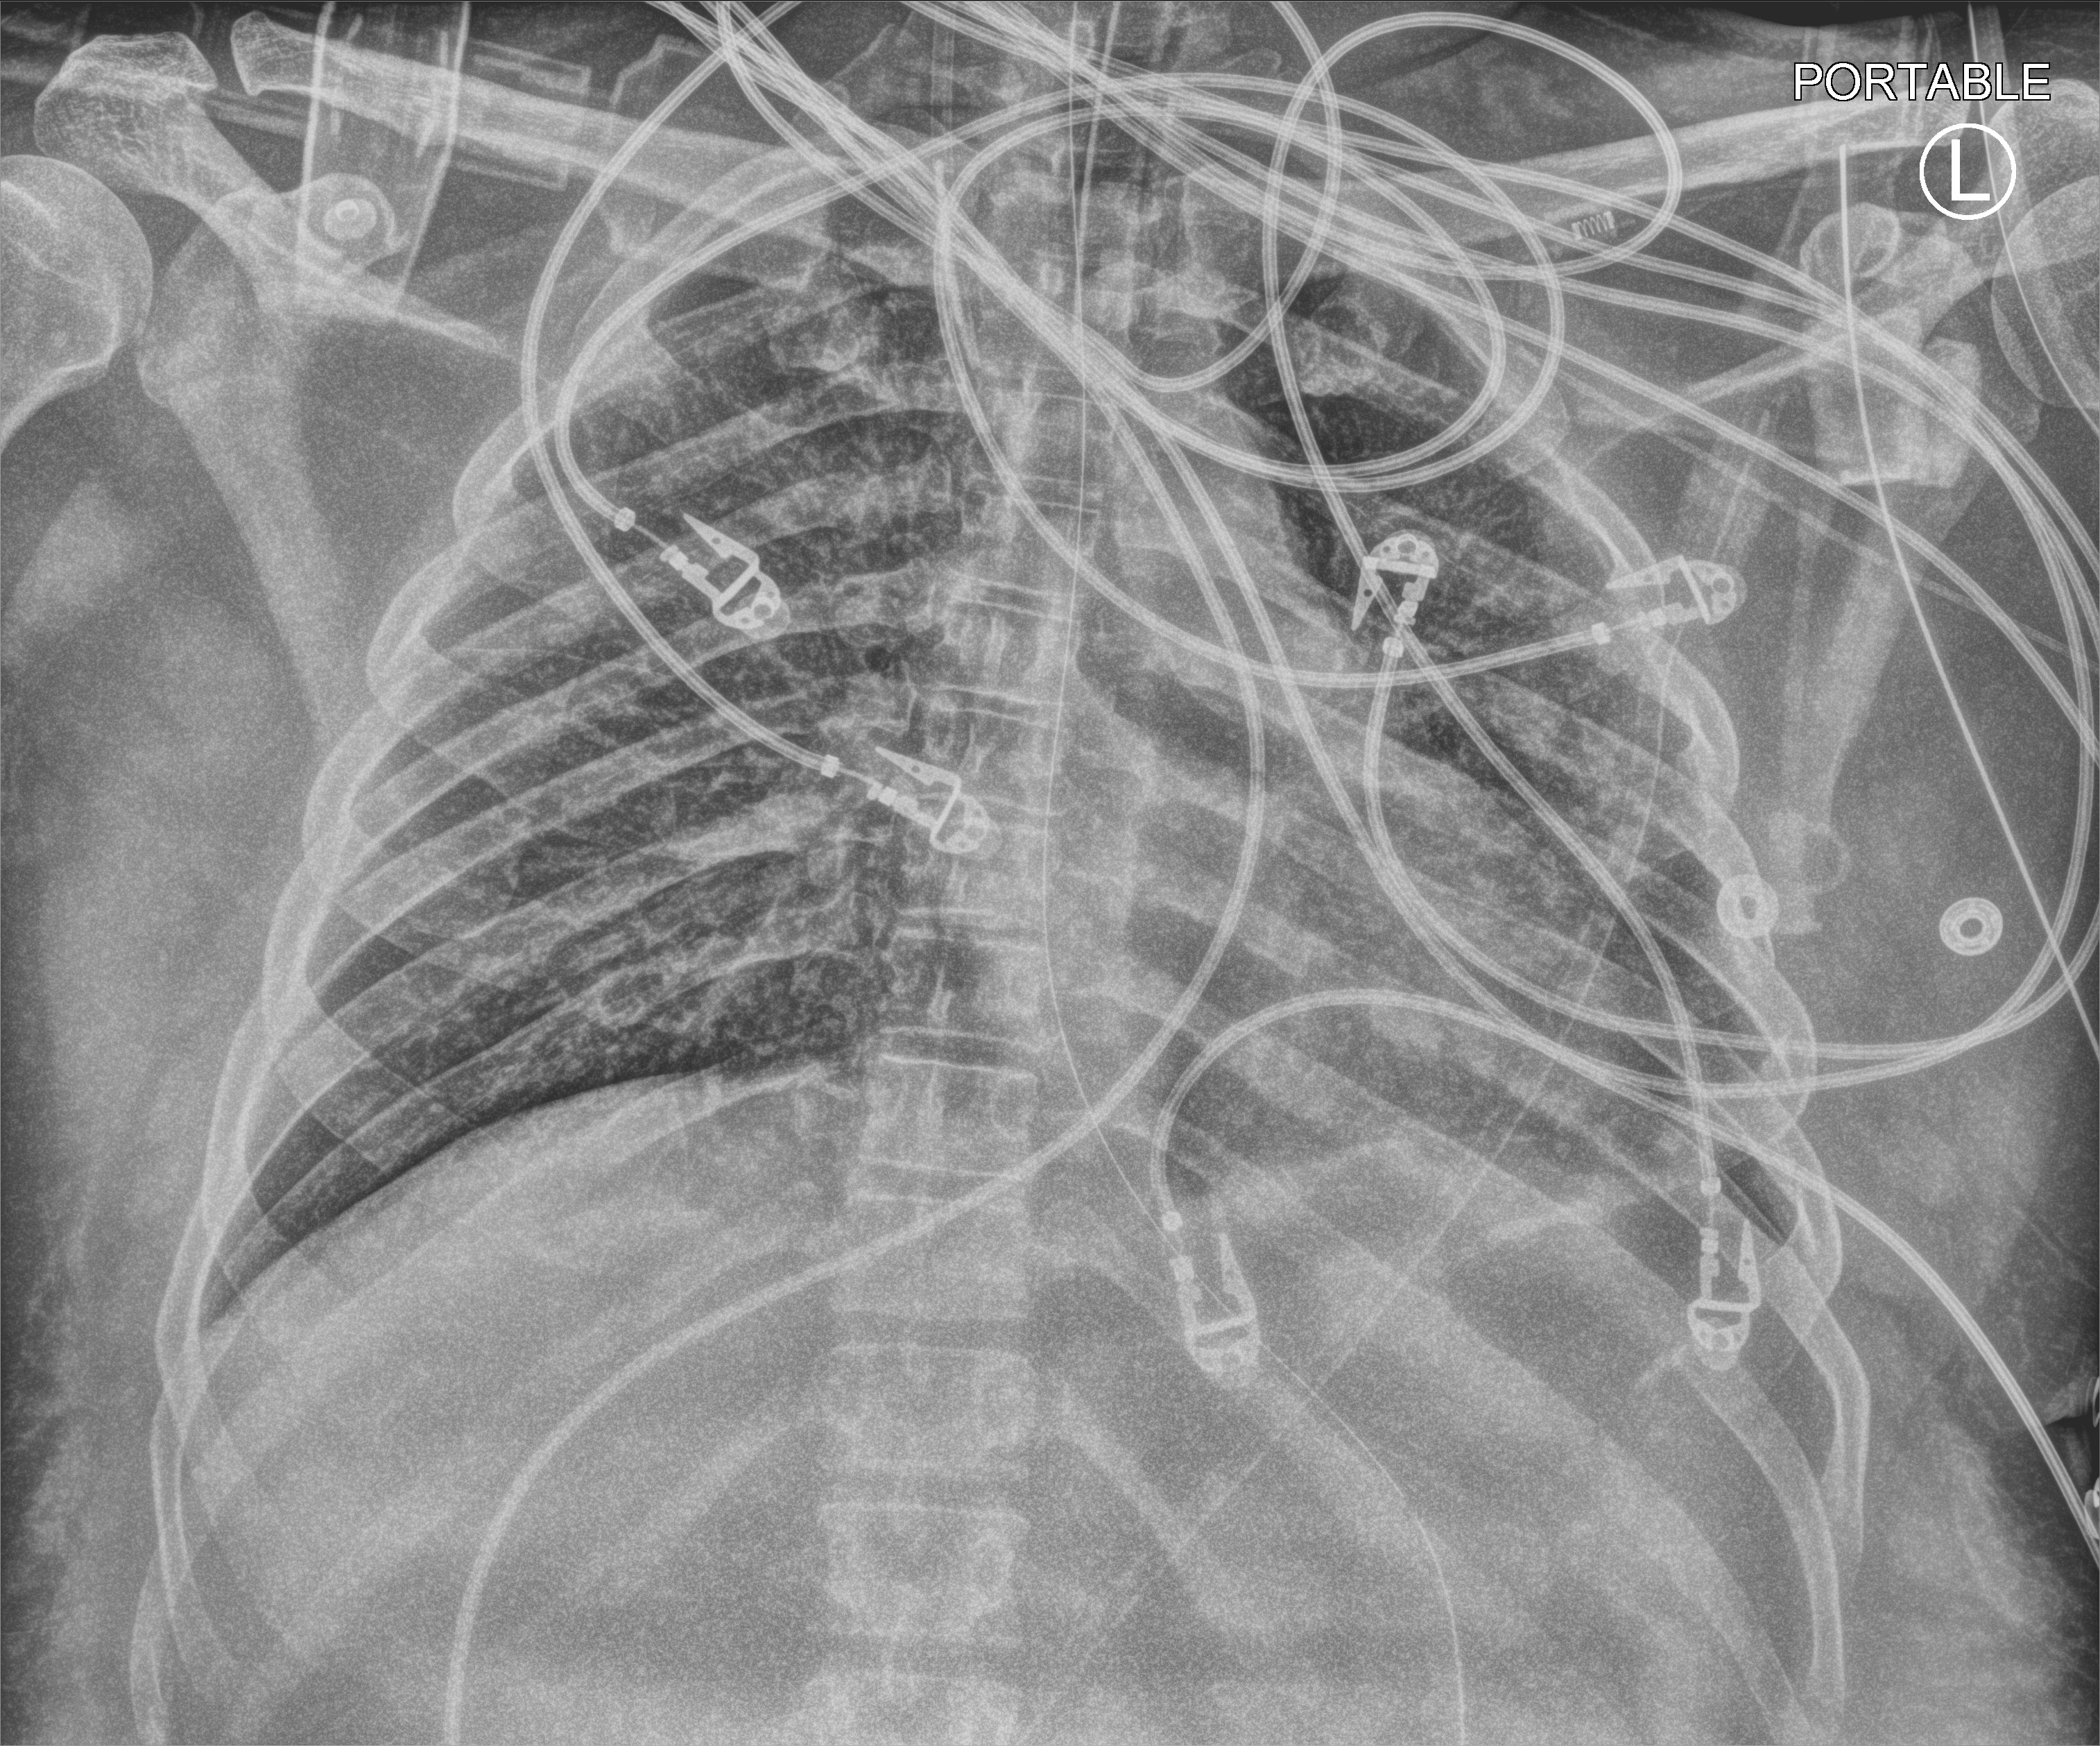
Portable chest radiograph; anteroposterior (AP) projection. Patient hospitalised with COVID-19, aged 18–59 years.
From the hospital-stay record, not from the radiograph (when in the stay this image was taken is not recorded): mechanically ventilated during this hospital stay: yes; other chronic lung disease (admission record): no.